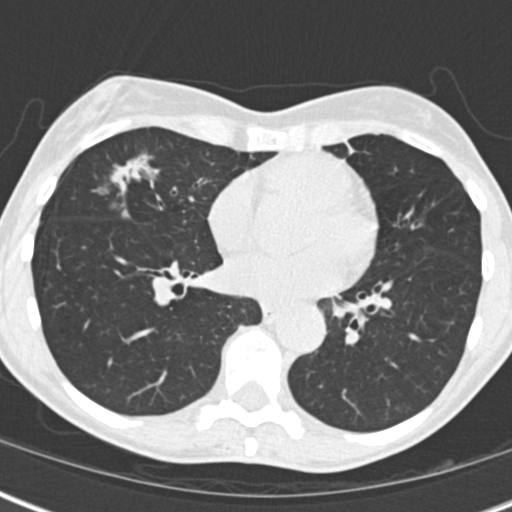
Low-dose screening chest CT, one axial slice; slice 74 of 173 in the series (ordered by position); reconstruction kernel B30f; 120 kVp; lung window (W 1500 / L -600 HU); 2 mm slice thickness; 512 × 512 image matrix, field of view 290 × 290 mm.
Annotated regions visible in this slice (outlined manually by an expert reader):
- lesion 1 (tumor, middle lobe of right lung): bounding box [x1, y1, x2, y2] px = [114, 157, 154, 189]